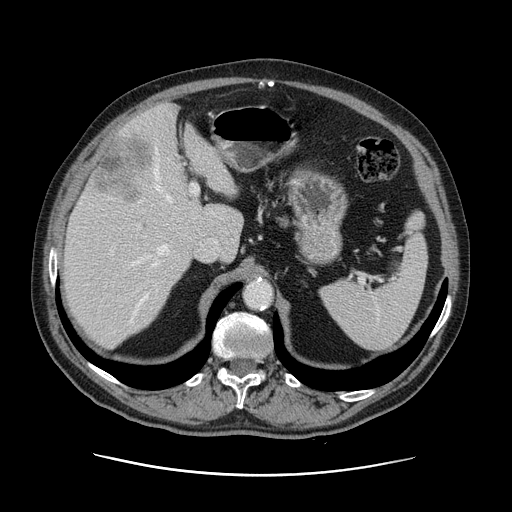
Contrast-enhanced abdominal CT, one axial slice; slice 86 of 141 in the series (ordered by position); 120 kVp; intravenous contrast given; soft-tissue window (W 400 / L 40 HU); 512 × 512 image matrix, field of view 395 × 395 mm. Male patient, age 72 years. Case-level facts recorded for this patient, not image findings: diagnosis: colorectal cancer liver metastases, imaged before liver resection; multiple liver metastases: yes; largest metastasis: 5.4 cm; disease in both lobes: yes.
Outlined on this slice (expert manual segmentation):
- hepatic veins: box from (x=131, y=159) to (x=171, y=322) px
- liver: (x=62, y=105)–(x=243, y=347)
- planned liver remnant (the part of the liver to remain after resection): (x=62, y=106)–(x=243, y=347)
- portal vein (with intrahepatic branches): (x=130, y=183)–(x=199, y=265)
- liver metastasis: (x=93, y=135)–(x=154, y=202)